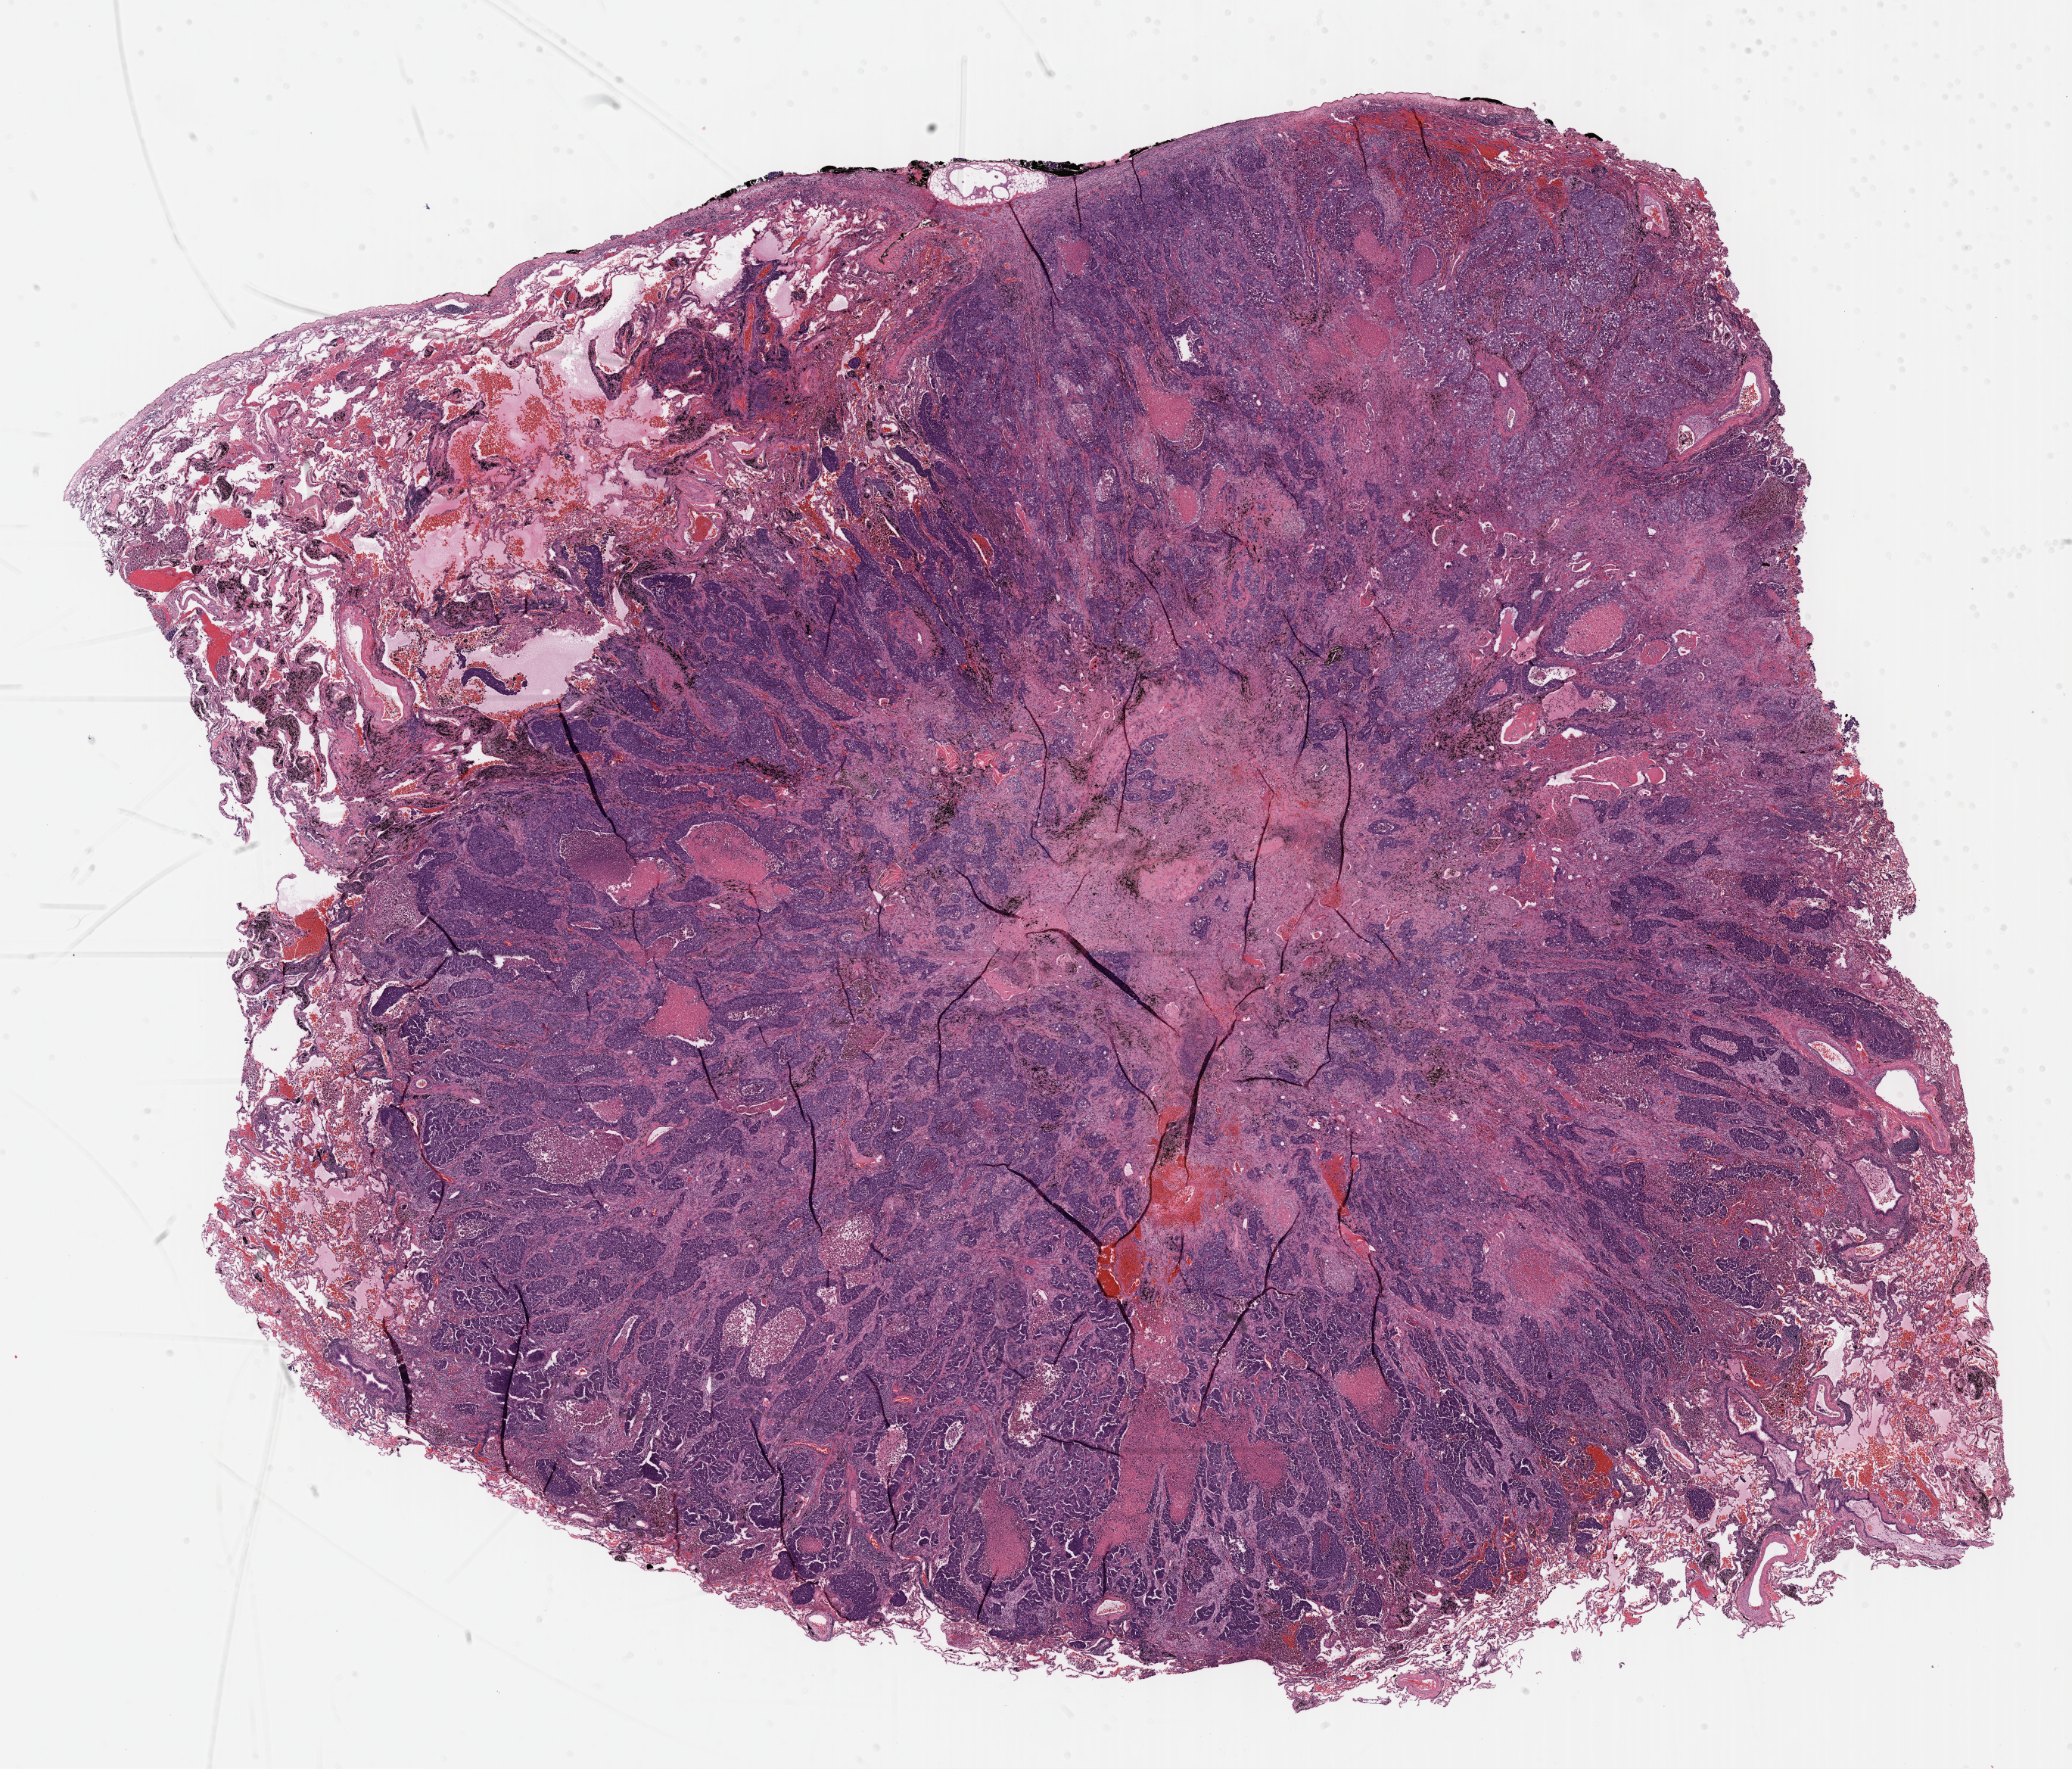
H&E-stained whole-slide image — a low-resolution overview of the entire scanned area, about 22.1 x 18.9 mm; FFPE section; sample: primary tumour, lung. Patient: female, age at initial diagnosis 52 years.
Diagnosis: Adenocarcinoma, NOS (lower lobe, lung).